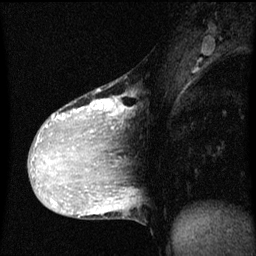
Breast MRI (dynamic contrast-enhanced), one sagittal slice; position 29 of 60 along the scan axis; dynamic contrast-enhanced series, image 2 of 3 at this slice position (ordered by acquisition); 1.5 T; TE 4.2 ms, TR 8 ms; 256 × 256 image matrix. Patient: female, 36 years.
Structures marked on this image (semi-automatically segmented with operator editing):
- analysis volume of interest (the breast-tissue region the enhancement analysis was run in; not a lesion): bounding box [x1, y1, x2, y2] px = [33, 88, 131, 169]
- tumour enhancement mask (voxels above the 70 % enhancement threshold inside the analysis volume of interest): [36, 98, 131, 167]